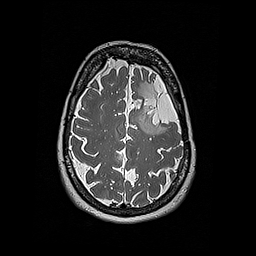
Brain MRI from a brain-tumour surgery series, one axial slice. Position 136 of 192 along the scan axis. 256 × 256 image matrix. From the clinical record (not read from this slice): histopathology: Oligodendroglioma; WHO grade: 2; IDH mutation: yes.
Annotated regions visible in this slice (expert manual segmentation):
- tumour: bounding box [x1, y1, x2, y2] px = [143, 115, 158, 134]